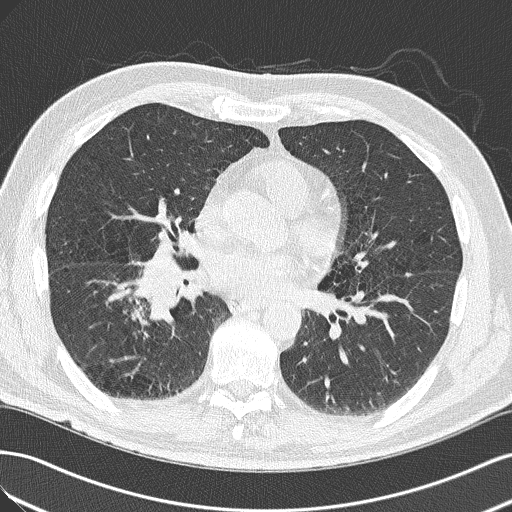
Chest CT (low-dose screening protocol), one axial image; first (baseline) screen; lung window (W 1500 / L -600 HU); 2 mm slice thickness; lung (sharp) reconstruction kernel (B50f); slice 85 of 143 in the series; 512 × 512 image matrix. Male, age 65 years at enrolment. Current smoker at enrolment.
Expert-annotated lung lesion, bounding box (x1, y1, x2, y2) in pixels: (103, 254, 208, 341). Screening reader's record for this exam (one nodule recorded; not confirmed to be the boxed lesion): non-calcified nodule or mass ≥4 mm, right upper lobe, 18 × 13 mm, spiculated (stellate) margins, soft tissue attenuation. Lung cancer was diagnosed 14 days after this screen: adenocarcinoma, NOS, right lower lobe, poorly differentiated (G3), stage IIIA (AJCC 6th edition), 40 mm at pathology.